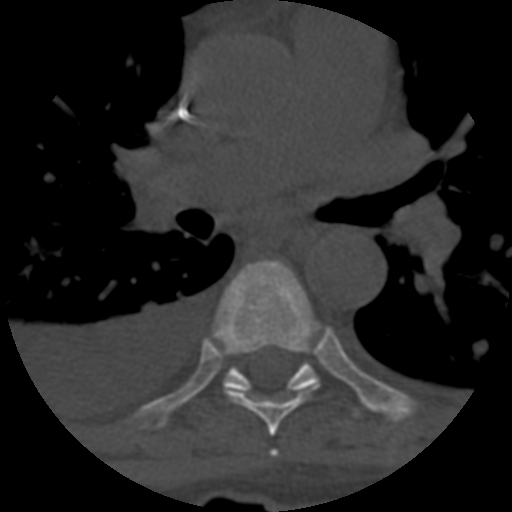
CT including the spine, one axial slice. One of 3 acquisitions stored at this slice position. Bone window (W 1800 / L 400 HU). 1.25 mm slice thickness. 512 × 512 image matrix. Patient age 55 years. From the clinical record (not read from this slice): primary cancer: colon; vertebrae with lytic lesions (as recorded): T12, L1, L5.
Outlined on this slice (semi-automatic segmentation, software-assisted and operator-edited):
- T5 vertebra: box from (x=271, y=451) to (x=277, y=456) px
- T6 vertebra: (x=213, y=260)–(x=320, y=436)
- T7 vertebra: (x=223, y=363)–(x=318, y=392)